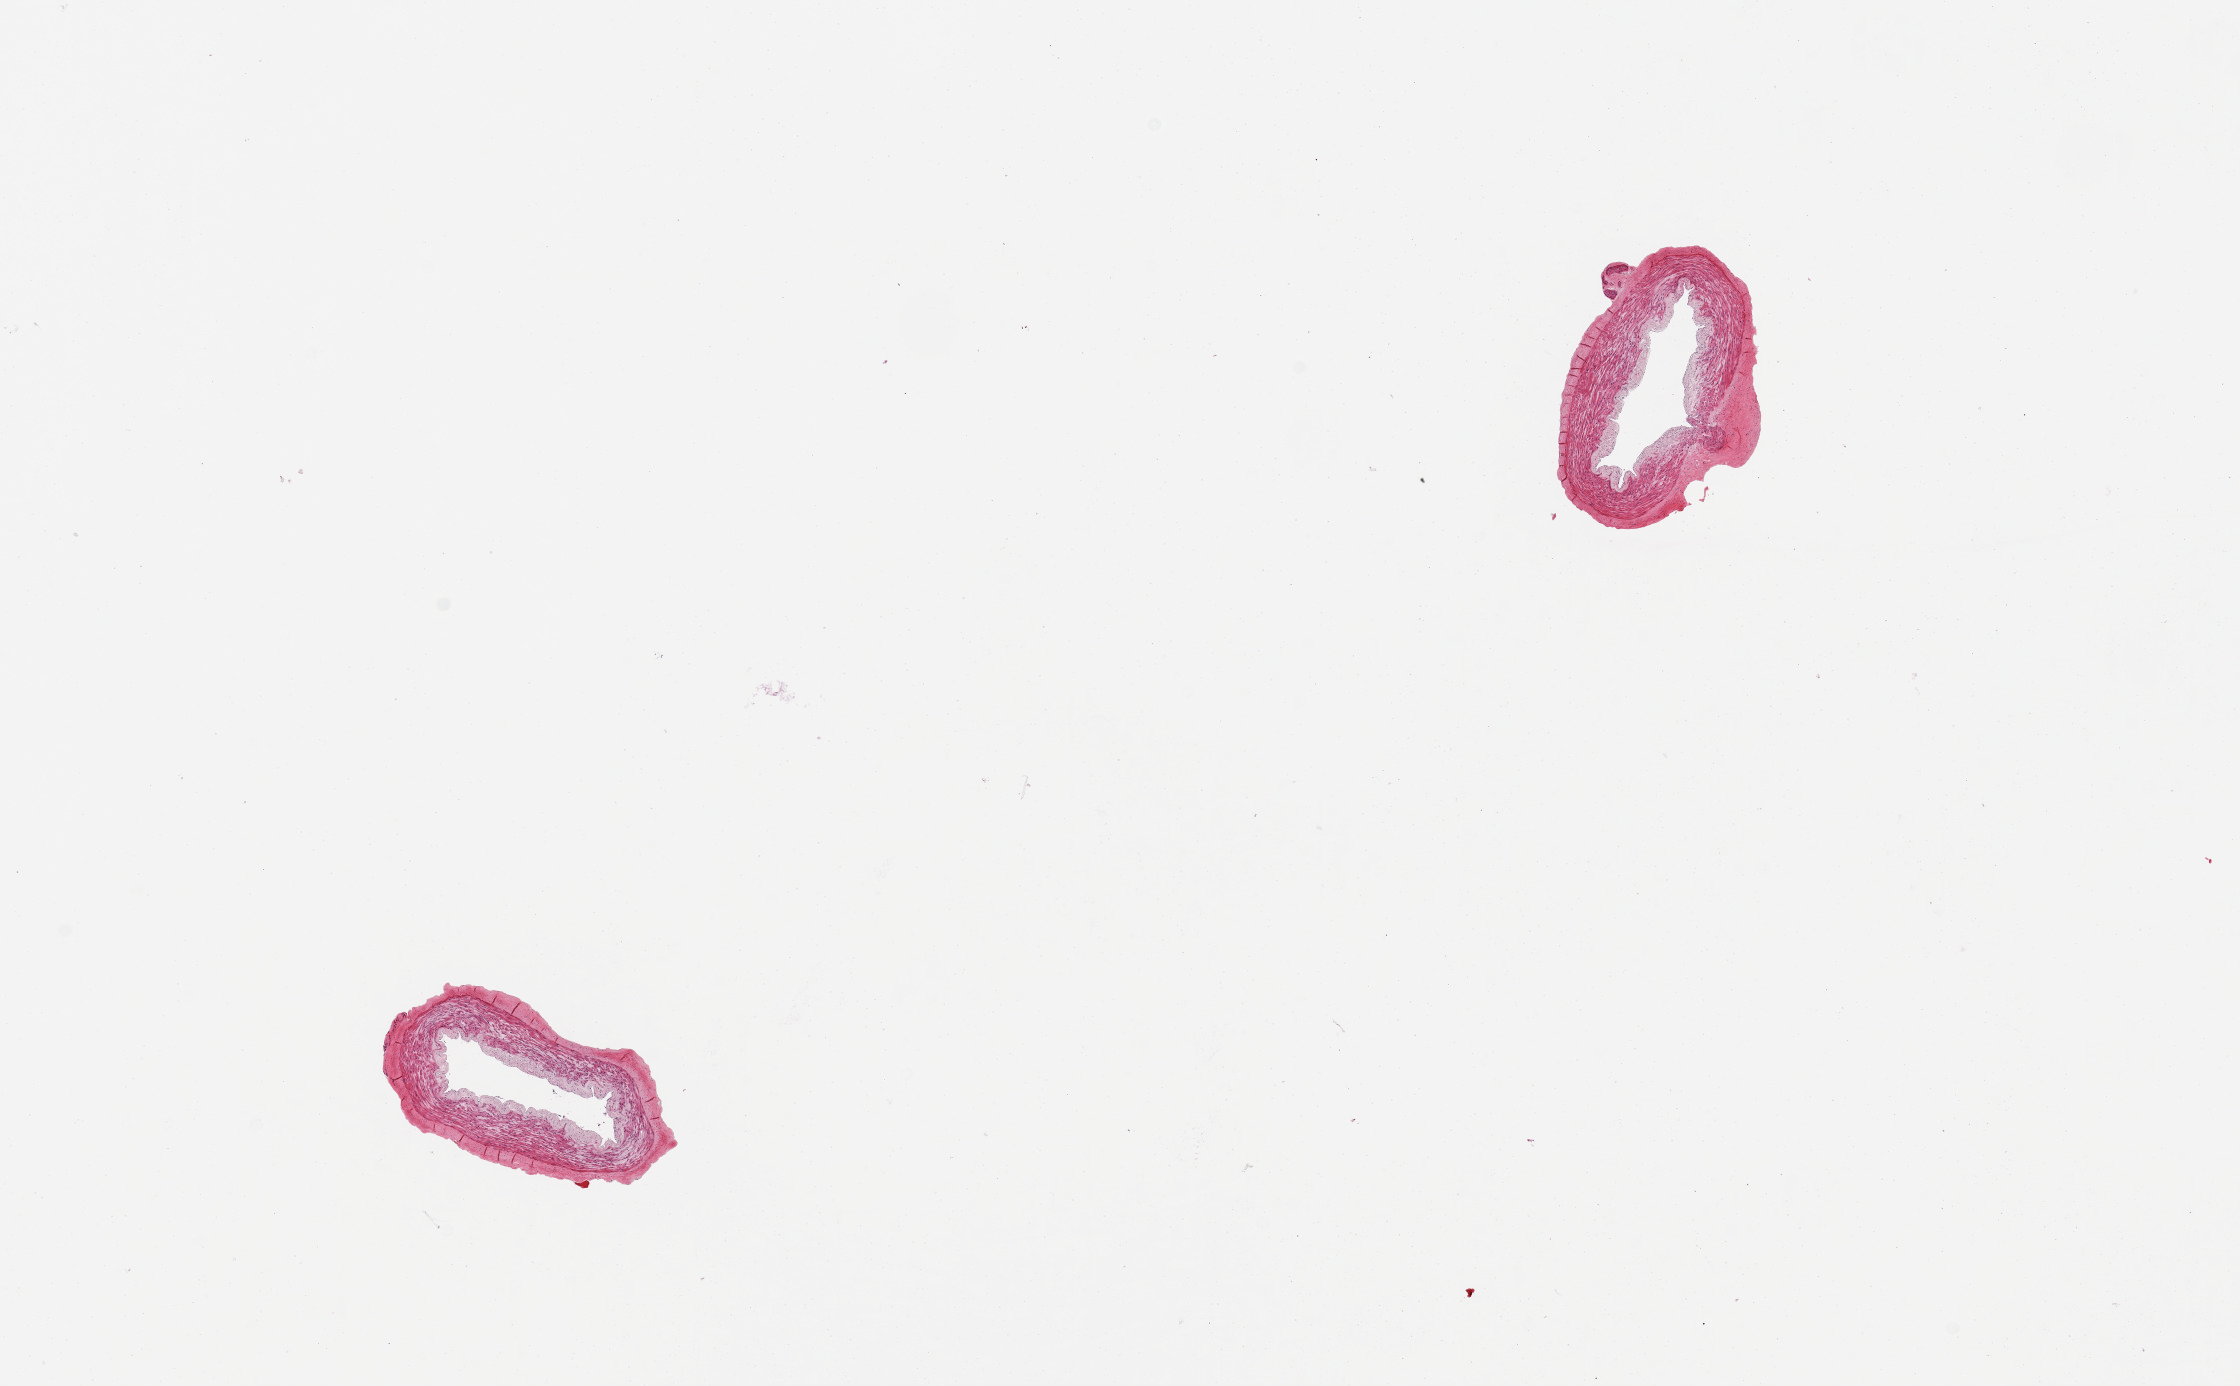
Whole-slide image, H&E stain, brightfield — low-resolution overview of the scanned area, about 17.7 x 11.0 mm (slide scanned at 20x). PAXgene-fixed paraffin-embedded (PFPE) section. Section of tibial artery (target tissue). Tissue donor sample.
* review note (as recorded): 2 pieces minimal adherent fibrous tissue/minute vessel, good specimens